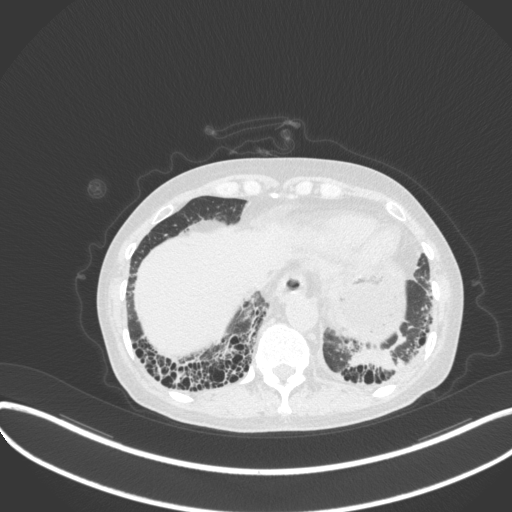
Chest CT, one axial slice; reconstruction kernel B31f; lung window (W 1500 / L -600 HU); 1 mm slice thickness; 512 × 512 image matrix, field of view 400 × 400 mm. Patient: female, 56 years. Case-level facts recorded for this patient, not image findings: clinical TNM (as recorded): T1 N0 M0.
Annotated regions visible in this slice (bounding box drawn by a radiologist):
- lung tumour (recorded histology: adenocarcinoma): bounding box [x1, y1, x2, y2] px = [344, 344, 404, 380]